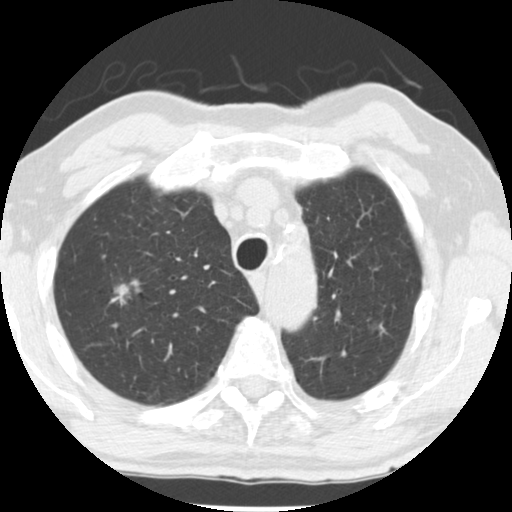
Low-dose screening chest CT, axial slice. Baseline screening round. Lung window (W 1500 / L -600 HU). 2.5 mm slice thickness. Slice 200 of 252 in the series. 512 × 512 image matrix, field of view 313 × 313 mm. Male participant, aged 69 years at enrolment. Former smoker at enrolment.
• Lesion marked by an expert reader, bounding box (x1, y1, x2, y2) in pixels: (92, 269, 153, 325).
• The screening reader recorded 2 non-calcified nodules or masses ≥4 mm on this exam (right upper lobe, left upper lobe); which of them this box marks is not recorded.
• Participant outcome: lung cancer diagnosed 105 days after this screen — adenocarcinoma, NOS, right upper lobe, well differentiated (G1), stage IA (AJCC 6th edition), 17 mm at pathology.